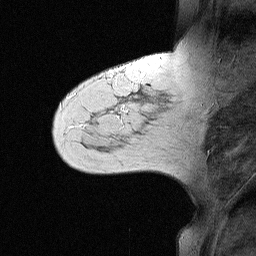
Breast MRI (dynamic contrast-enhanced), one sagittal slice. Slice 16 of 64 in the series (ordered by position). Dynamic contrast-enhanced study with each time point stored as its own series, time point 2 of 3 at this slice position (early post-contrast, ordered by acquisition time). 1.5 T. TE 4.5 ms, TR 11 ms. 256 × 256 image matrix, field of view 200 × 200 mm. Female patient, age 55 years. Case-level facts recorded for this patient, not image findings: setting: breast cancer imaged before/during neoadjuvant chemotherapy; receptor status: triple-negative.
Outlined on this slice (semi-automatic segmentation, software-assisted and operator-edited):
- analysis volume of interest (the breast-tissue region the enhancement analysis was run in; not a lesion): bounding box (x1, y1, x2, y2) in pixels: (71, 63, 147, 145)
- tumour enhancement mask (voxels above the 90 % enhancement threshold inside the analysis volume of interest): (112, 109, 121, 114)